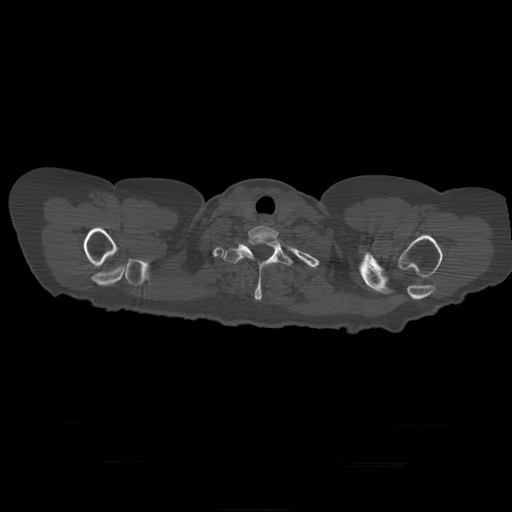
CT including the spine, one axial slice; position 380 of 399 along the scan axis; reconstruction kernel STANDARD; bone window (W 1800 / L 400 HU); 1.25 mm slice thickness; 512 × 512 image matrix, field of view 450 × 450 mm. Patient age 41 years. From the clinical record (not read from this slice): primary cancer: breast.
Annotated regions visible in this slice (semi-automatically segmented with operator editing):
- T1 vertebra: bounding box <239,226,279,263> (left, top, right, bottom; pixels)
- T2 vertebra: <223,238,294,300>